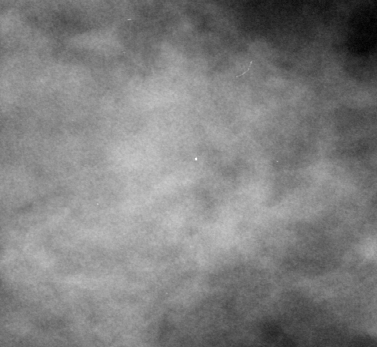
Crop from a digitized film mammogram around one marked abnormality; left breast; CC view.
Marked abnormality: mass, shape irregular, margins ill defined; BI-RADS assessment category 4; subtlety rating 2 on a 1 (subtle) to 5 (obvious) scale; pathology (as recorded): benign.